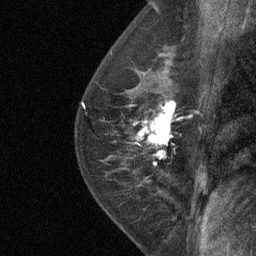
Breast MRI (dynamic contrast-enhanced), one sagittal slice. Slice 43 of 64 in the series (ordered by position). Dynamic contrast-enhanced study with each time point stored as its own series, time point 2 of 4 at this slice position (early post-contrast, ordered by acquisition time). 1.5 T. TE 4.8 ms, TR 27 ms. 2 mm slice thickness. 256 × 256 image matrix, field of view 180 × 180 mm. Female patient, age 50 years. From the clinical record (not read from this slice): setting: breast cancer imaged before/during neoadjuvant chemotherapy; receptor status: HER2-positive.
Structures marked on this image (semi-automatic segmentation, software-assisted and operator-edited):
- analysis volume of interest (the breast-tissue region the enhancement analysis was run in; not a lesion): bounding box <123,91,187,177> (left, top, right, bottom; pixels)
- tumour enhancement mask (voxels above the 90 % enhancement threshold inside the analysis volume of interest): <135,101,176,164>